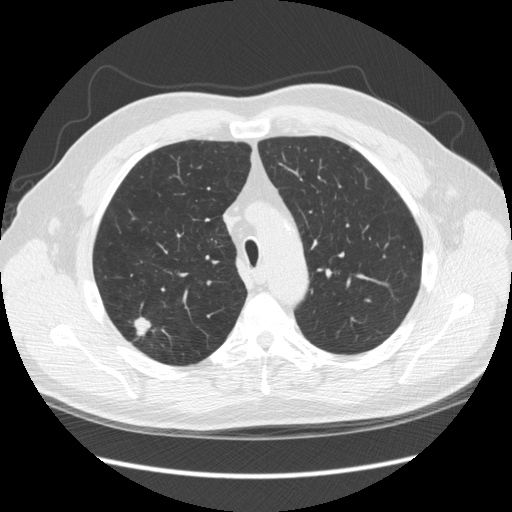
Low-dose screening chest CT, one axial slice. Position 186 of 248 along the scan axis. Lung window (W 1500 / L -600 HU). 2.5 mm slice thickness. 512 × 512 image matrix.
Annotated regions visible in this slice (manually delineated by an expert):
- lesion 1 (tumor, upper lobe of right lung): bounding box [x1, y1, x2, y2] px = [134, 317, 151, 336]